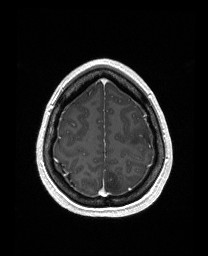
Brain MRI from a brain-tumour surgery series, one axial slice; slice 131 of 176 in the series (ordered by position); T1-weighted post-contrast; 208 × 256 image matrix. Case-level facts recorded for this patient, not image findings: histopathology: Astrocytoma; WHO grade: 3; IDH mutation: yes; tumour location: Left Frontal.
Outlined on this slice (expert manual segmentation):
- tumour: bounding box <130,124,153,148> (left, top, right, bottom; pixels)